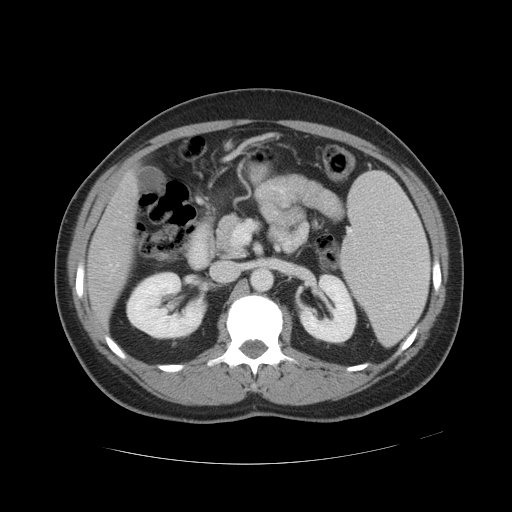
Contrast-enhanced abdominal CT, one axial slice; position 24 of 49 along the scan axis; 120 kVp; intravenous contrast given; soft-tissue window (W 400 / L 40 HU); 5 mm slice thickness; 512 × 512 image matrix, field of view 422 × 422 mm. Male patient, age 42 years. Case-level facts recorded for this patient, not image findings: diagnosis: colorectal cancer liver metastases, imaged before liver resection; multiple liver metastases: yes; largest metastasis: 2.8 cm; disease in both lobes: yes.
Outlined on this slice (outlined manually by an expert reader):
- hepatic veins: box from (x=110, y=212) to (x=120, y=267) px
- liver: (x=90, y=176)–(x=135, y=323)
- planned liver remnant (the part of the liver to remain after resection): (x=90, y=234)–(x=130, y=323)
- portal vein (with intrahepatic branches): (x=117, y=263)–(x=119, y=266)